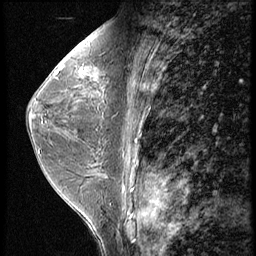
Breast MRI (dynamic contrast-enhanced), one sagittal slice; position 29 of 56 along the scan axis; 3 images stored at this slice position (order not interpretable as contrast timing); 1.5 T; TE 4.2 ms, TR 9 ms; 2.5 mm slice thickness; 256 × 256 image matrix. Patient: female, 44 years. From the clinical record (not read from this slice): setting: breast cancer imaged before/during neoadjuvant chemotherapy; receptor status: triple-negative.
Structures marked on this image (semi-automatically segmented with operator editing):
- analysis volume of interest (the breast-tissue region the enhancement analysis was run in; not a lesion): bounding box [x1, y1, x2, y2] px = [71, 54, 112, 99]
- tumour enhancement mask (voxels above the 140 % enhancement threshold inside the analysis volume of interest): [79, 68, 86, 74]